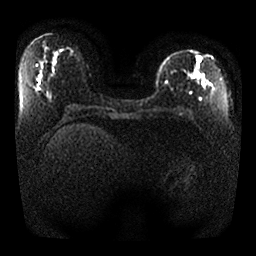
Breast MRI, one axial slice. Position 10 of 25 along the scan axis. Diffusion-weighted series; image 2 of 4 stored at this slice position (different b-values; order by instance number). 1.5 T. 4 mm slice thickness. 256 × 256 image matrix, field of view 330 × 330 mm. Female patient.
Annotated regions visible in this slice (outlined manually by an expert reader):
- tumour on diffusion-weighted imaging: bounding box <201,72,213,89> (left, top, right, bottom; pixels)